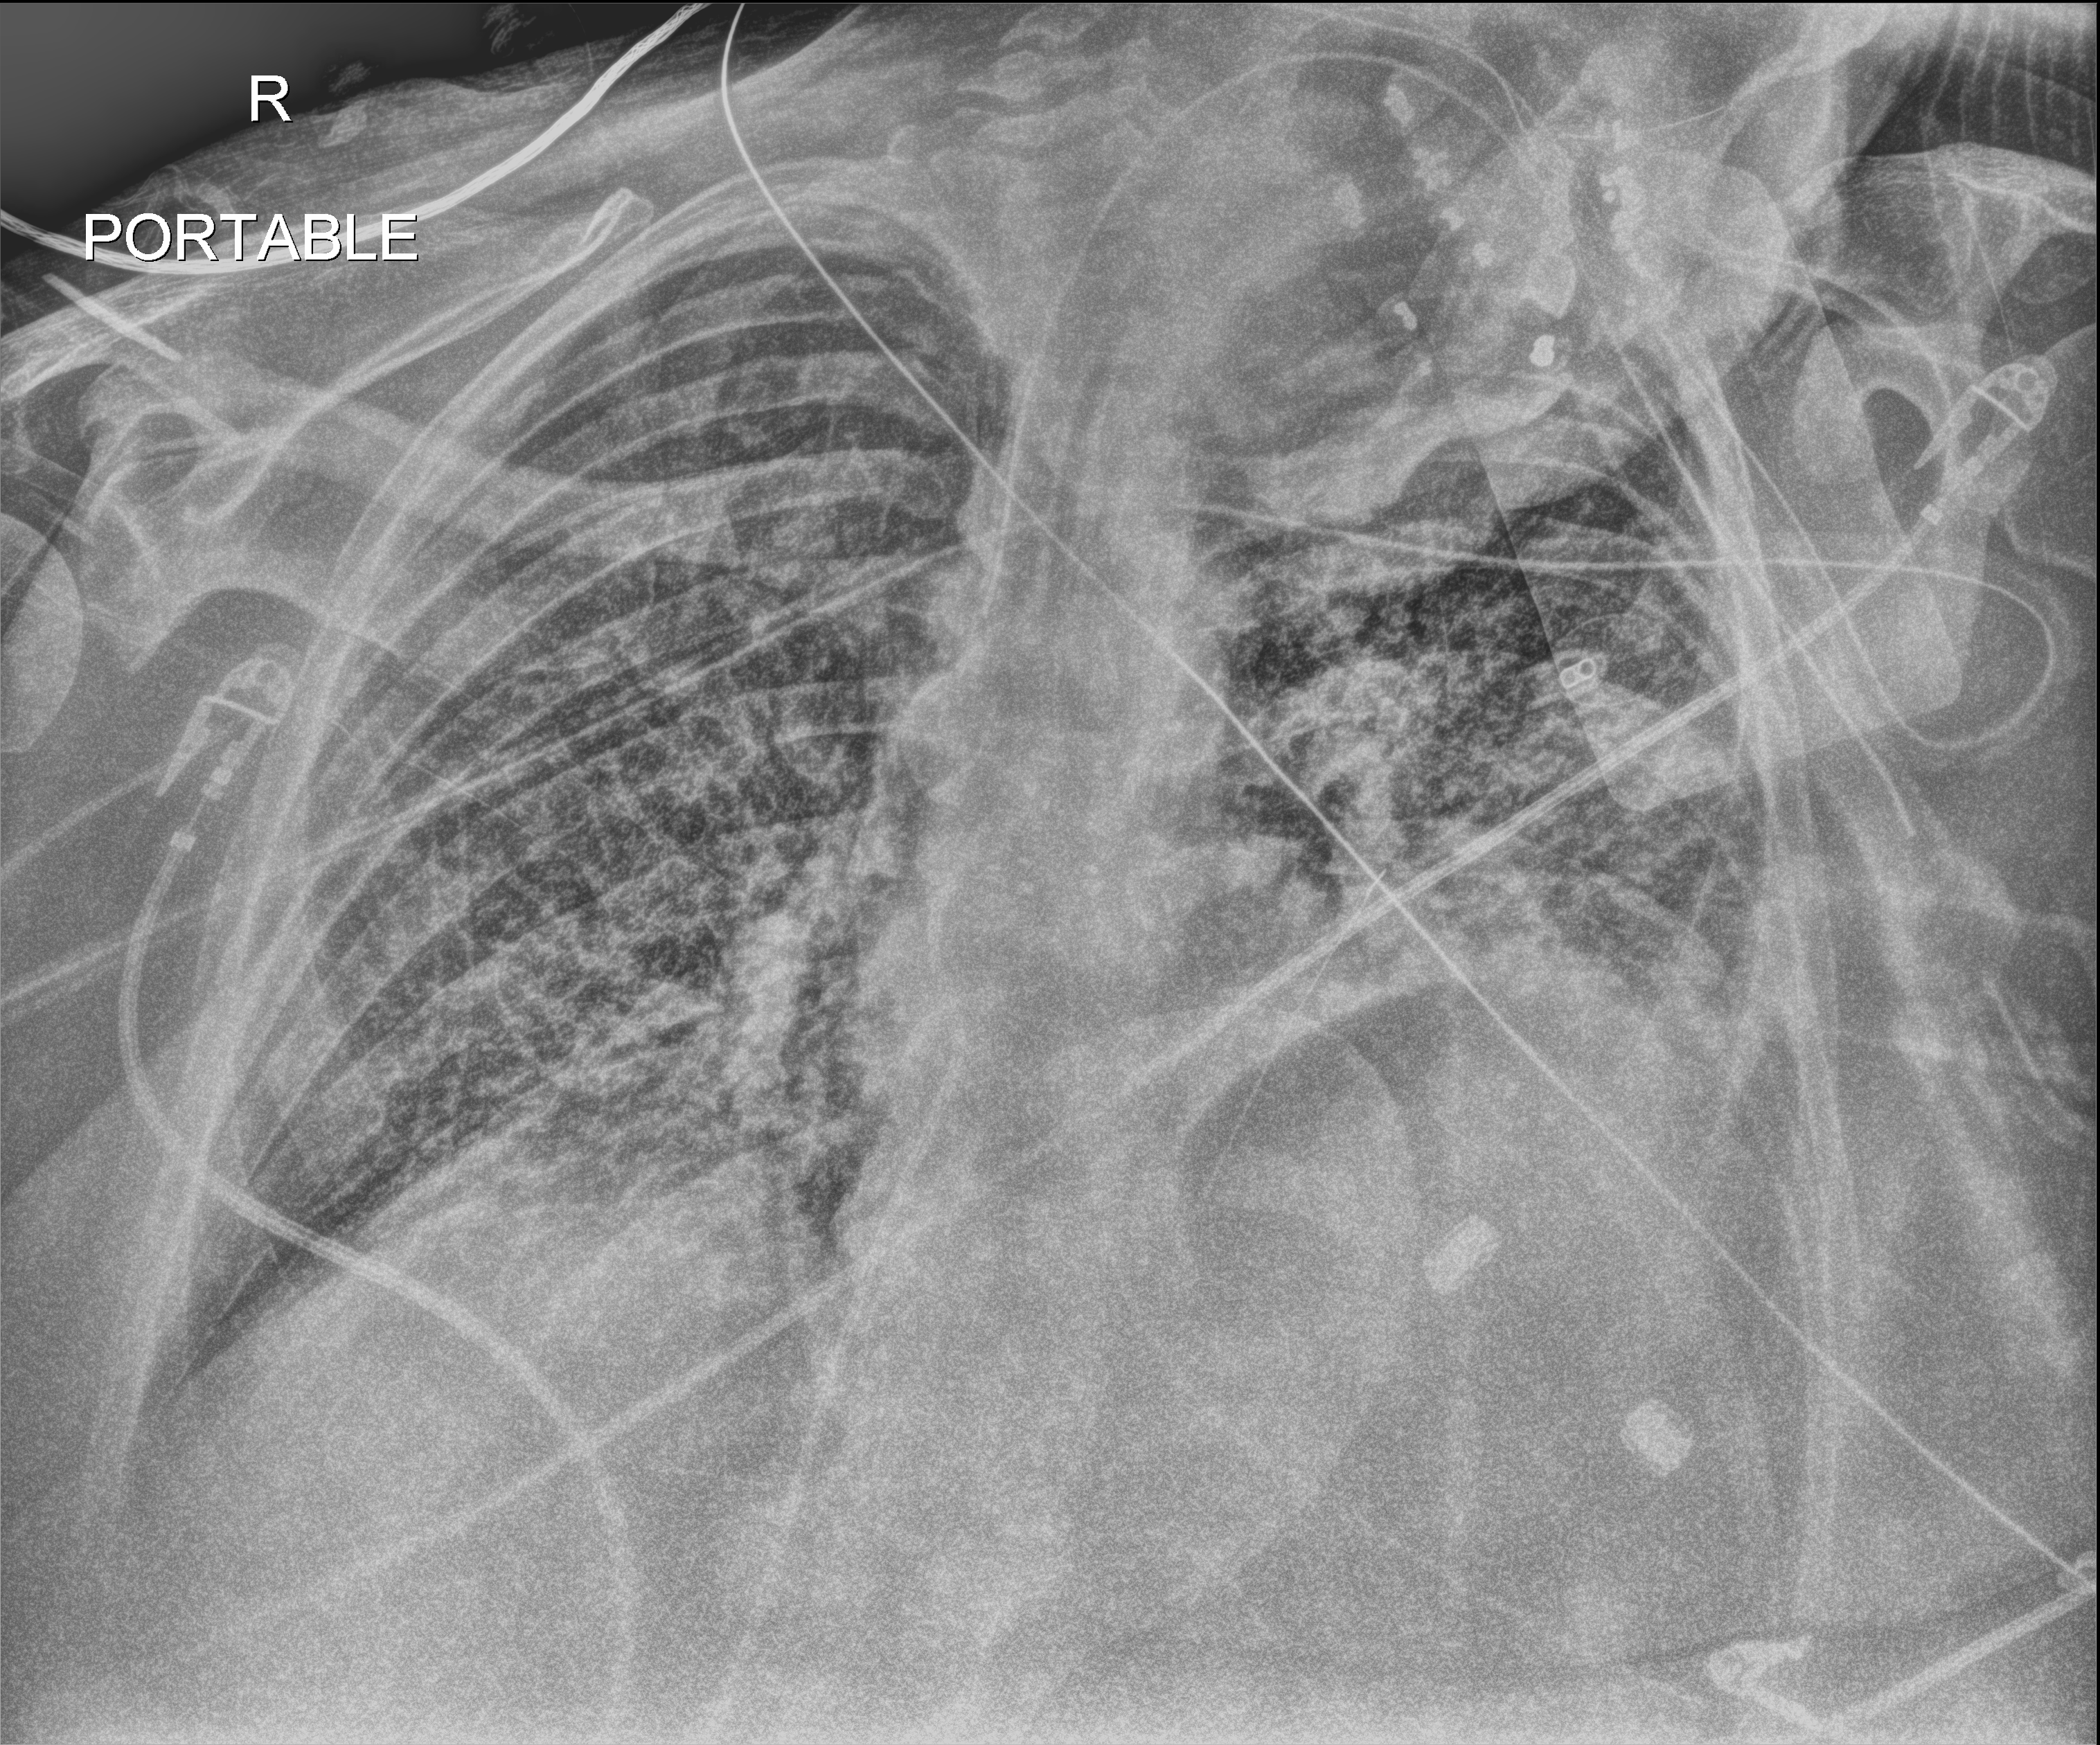
Chest X-ray (portable), anteroposterior (AP) projection. Patient hospitalised with COVID-19, aged 18–59 years.
From the hospital-stay record, not from the radiograph (when in the stay this image was taken is not recorded): mechanically ventilated during this hospital stay: yes.